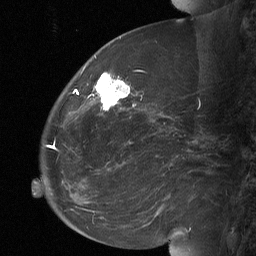
Breast MRI (dynamic contrast-enhanced), one sagittal slice; dynamic contrast-enhanced study with each time point stored as its own series, time point 2 of 3 at this slice position (early post-contrast, ordered by acquisition time); 1.5 T; TE 4.8 ms, TR 27 ms; 256 × 256 image matrix, field of view 200 × 200 mm. Patient: female, 60 years. From the clinical record (not read from this slice): setting: breast cancer imaged before/during neoadjuvant chemotherapy; receptor status: HR-positive, HER2-negative.
Outlined on this slice (semi-automatically segmented with operator editing):
- analysis volume of interest (the breast-tissue region the enhancement analysis was run in; not a lesion): bounding box (x1, y1, x2, y2) in pixels: (92, 70, 134, 112)
- tumour enhancement mask (voxels above the 90 % enhancement threshold inside the analysis volume of interest): (96, 73, 130, 110)